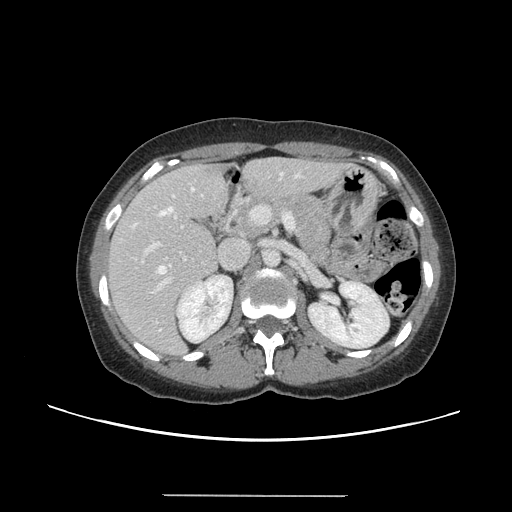
Contrast-enhanced abdominal CT, one axial slice. Slice 76 of 144 in the series (ordered by position). 120 kVp. Intravenous contrast given. Soft-tissue window (W 400 / L 40 HU). 2.5 mm slice thickness. 512 × 512 image matrix. Female patient, age 53 years. From the clinical record (not read from this slice): diagnosis: colorectal cancer liver metastases, imaged before liver resection; multiple liver metastases: yes; largest metastasis: 1.1 cm; disease in both lobes: no.
Annotated regions visible in this slice (outlined manually by an expert reader):
- hepatic veins: bounding box (x1, y1, x2, y2) in pixels: (157, 172, 298, 274)
- liver: (108, 159, 343, 355)
- planned liver remnant (the part of the liver to remain after resection): (109, 159, 319, 299)
- portal vein (with intrahepatic branches): (135, 206, 295, 294)